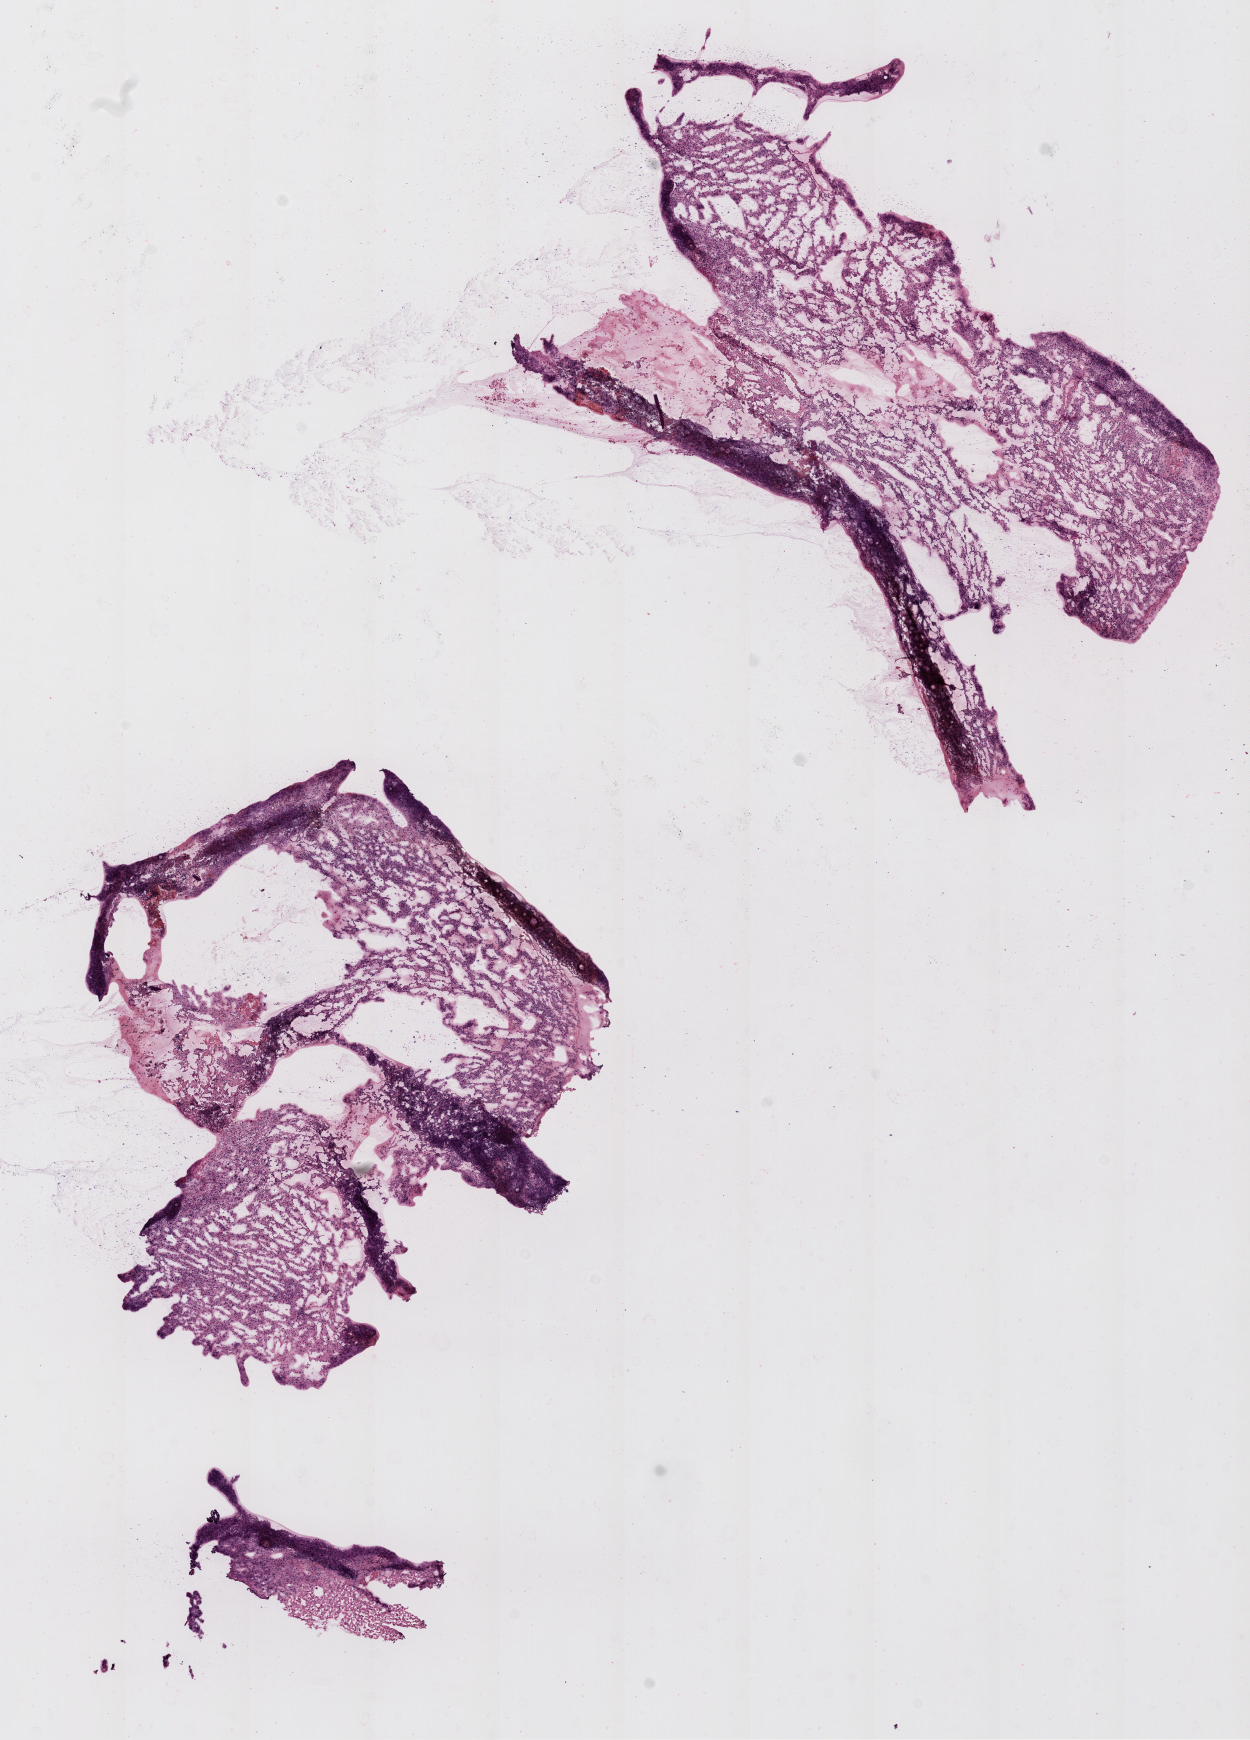
Hematoxylin and eosin (H&E) stained whole-slide image, a low-resolution overview of the entire scanned area, about 10.0 x 14.0 mm (acquisition: 20x scan). Frozen section from the top of the tissue portion. Sample: primary tumour, brain. Patient: male, age at initial diagnosis 74 years. Pathologist review of this section (percent, as recorded): tumour cells 100%, tumour nuclei 80%, normal cells 0%, stromal cells 0%, necrosis 0%.
• diagnosis: Glioblastoma